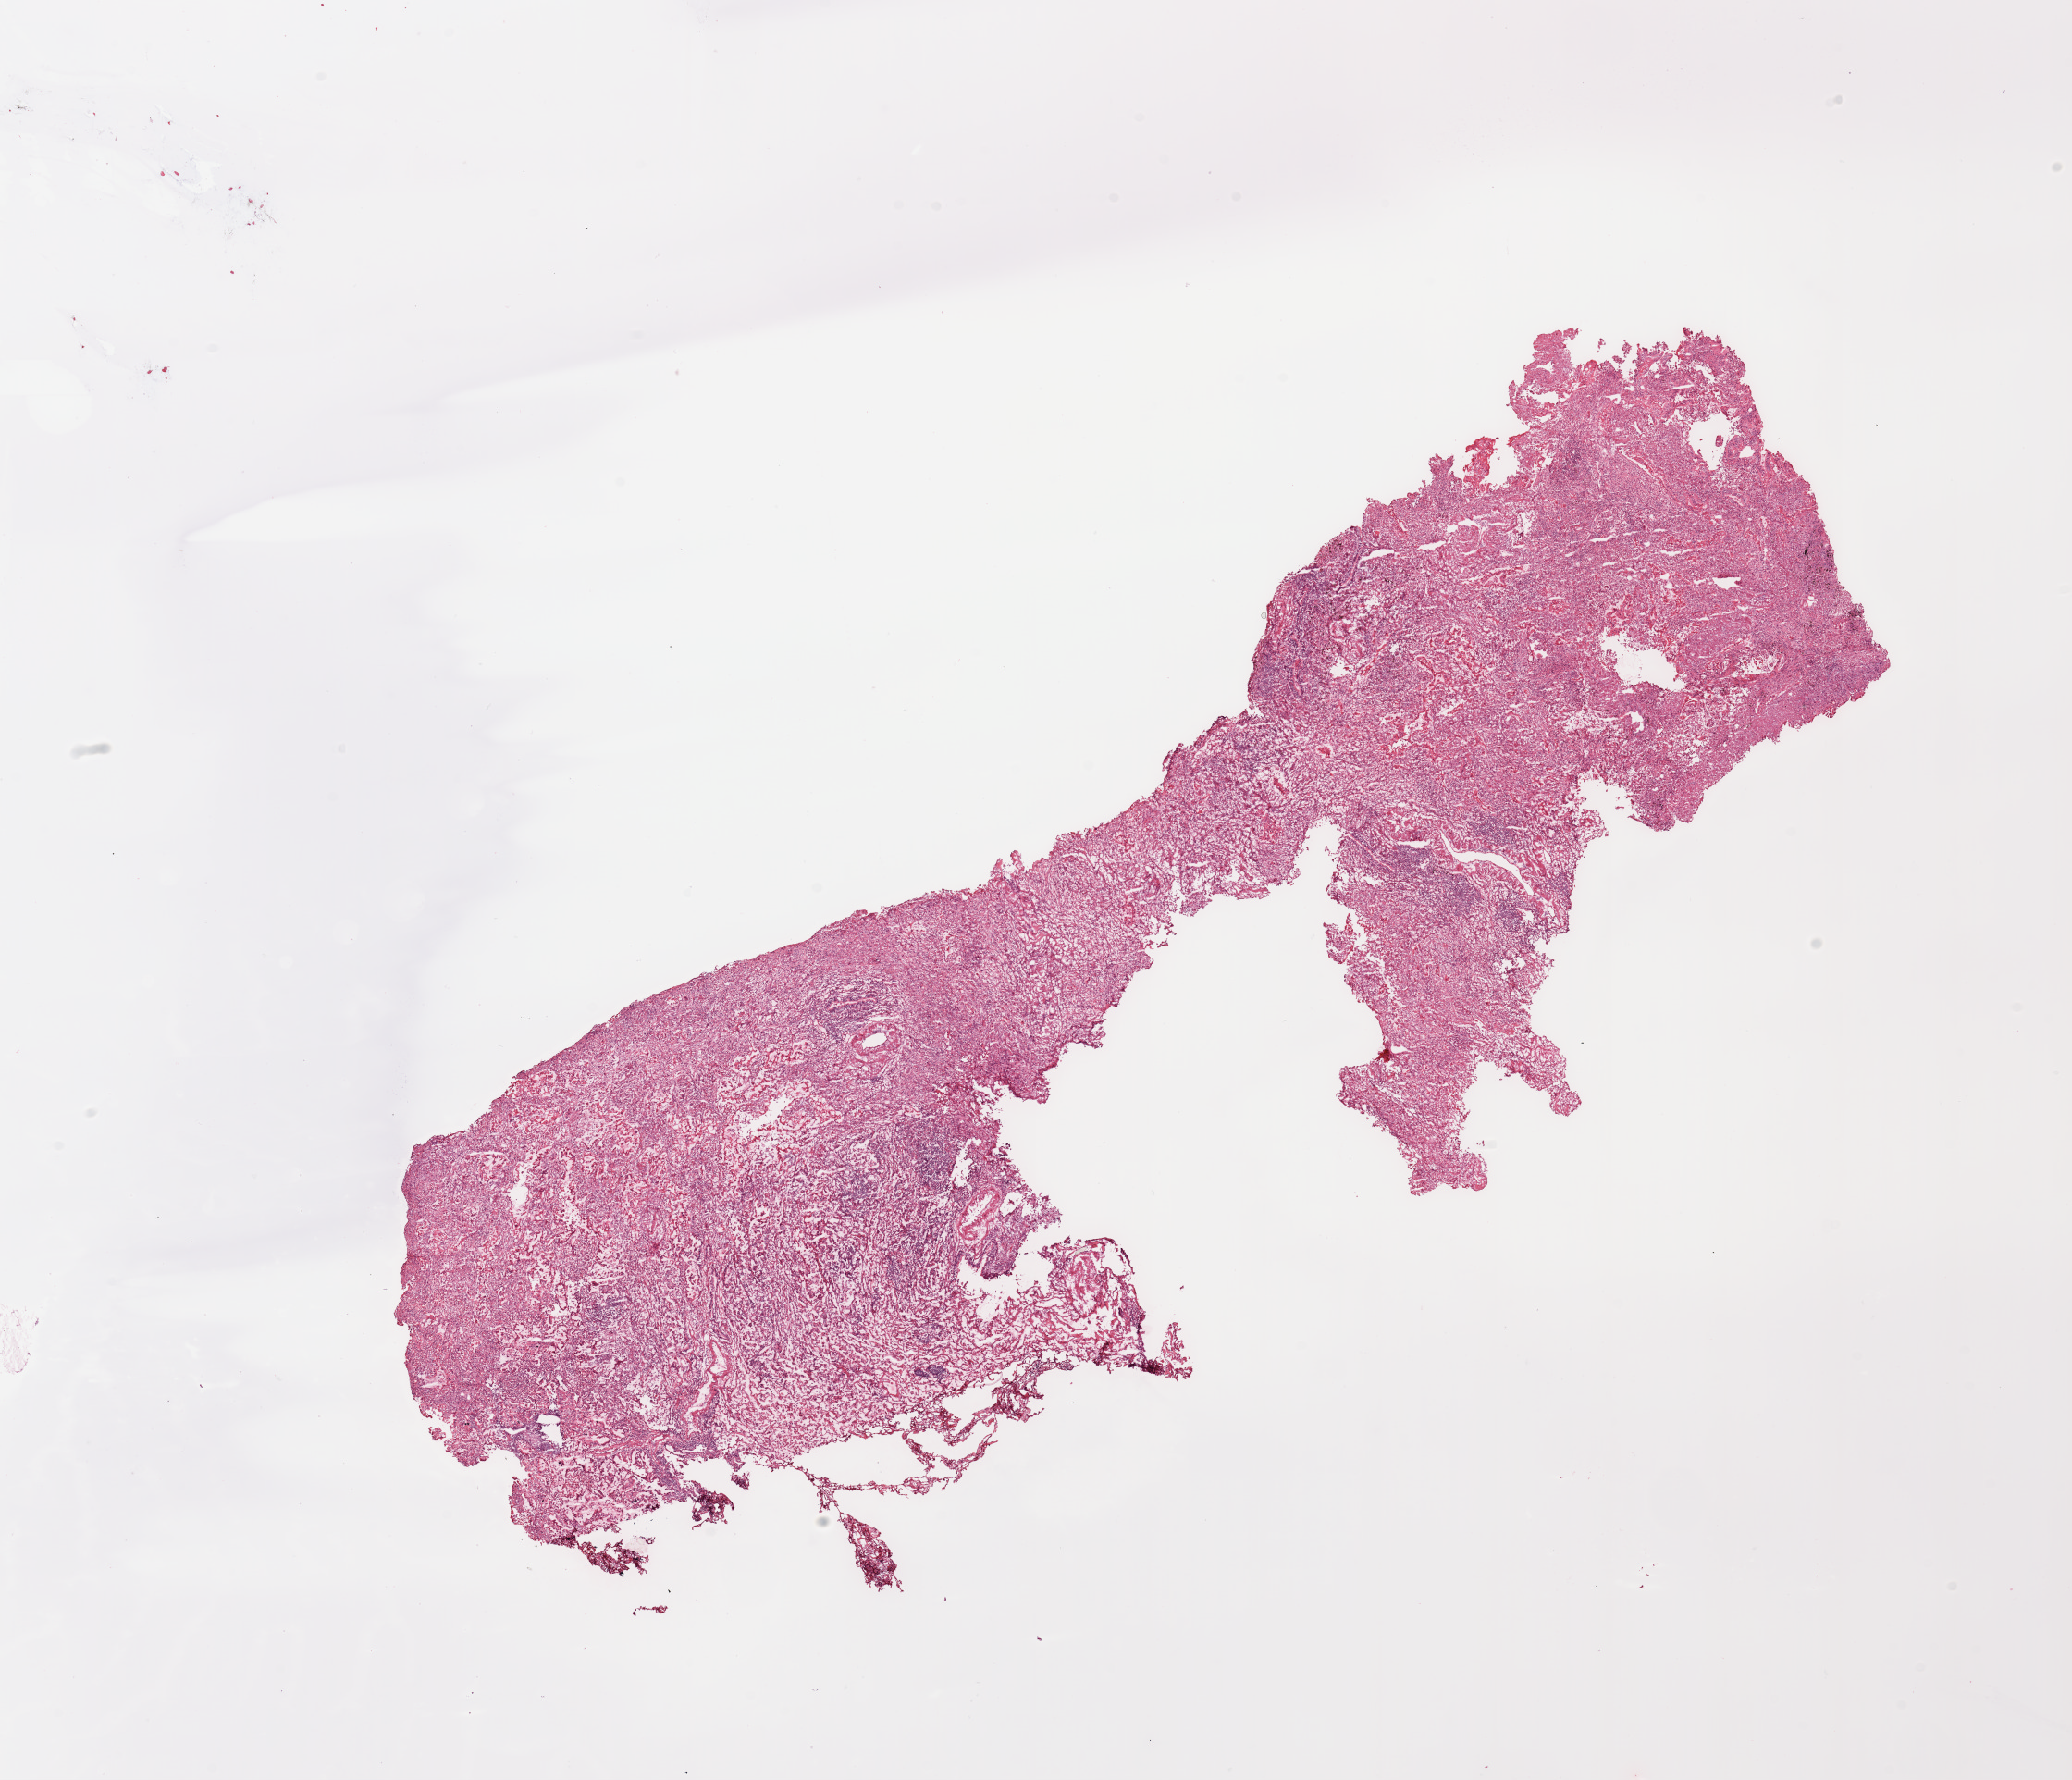
Digitized H&E-stained tissue section (whole slide) — low-resolution overview of the scanned area, about 17.7 x 15.2 mm (from a 20x scan). Lung, tumour tissue. 79-year-old male patient.
Diagnosis: Adenocarcinoma, NOS.